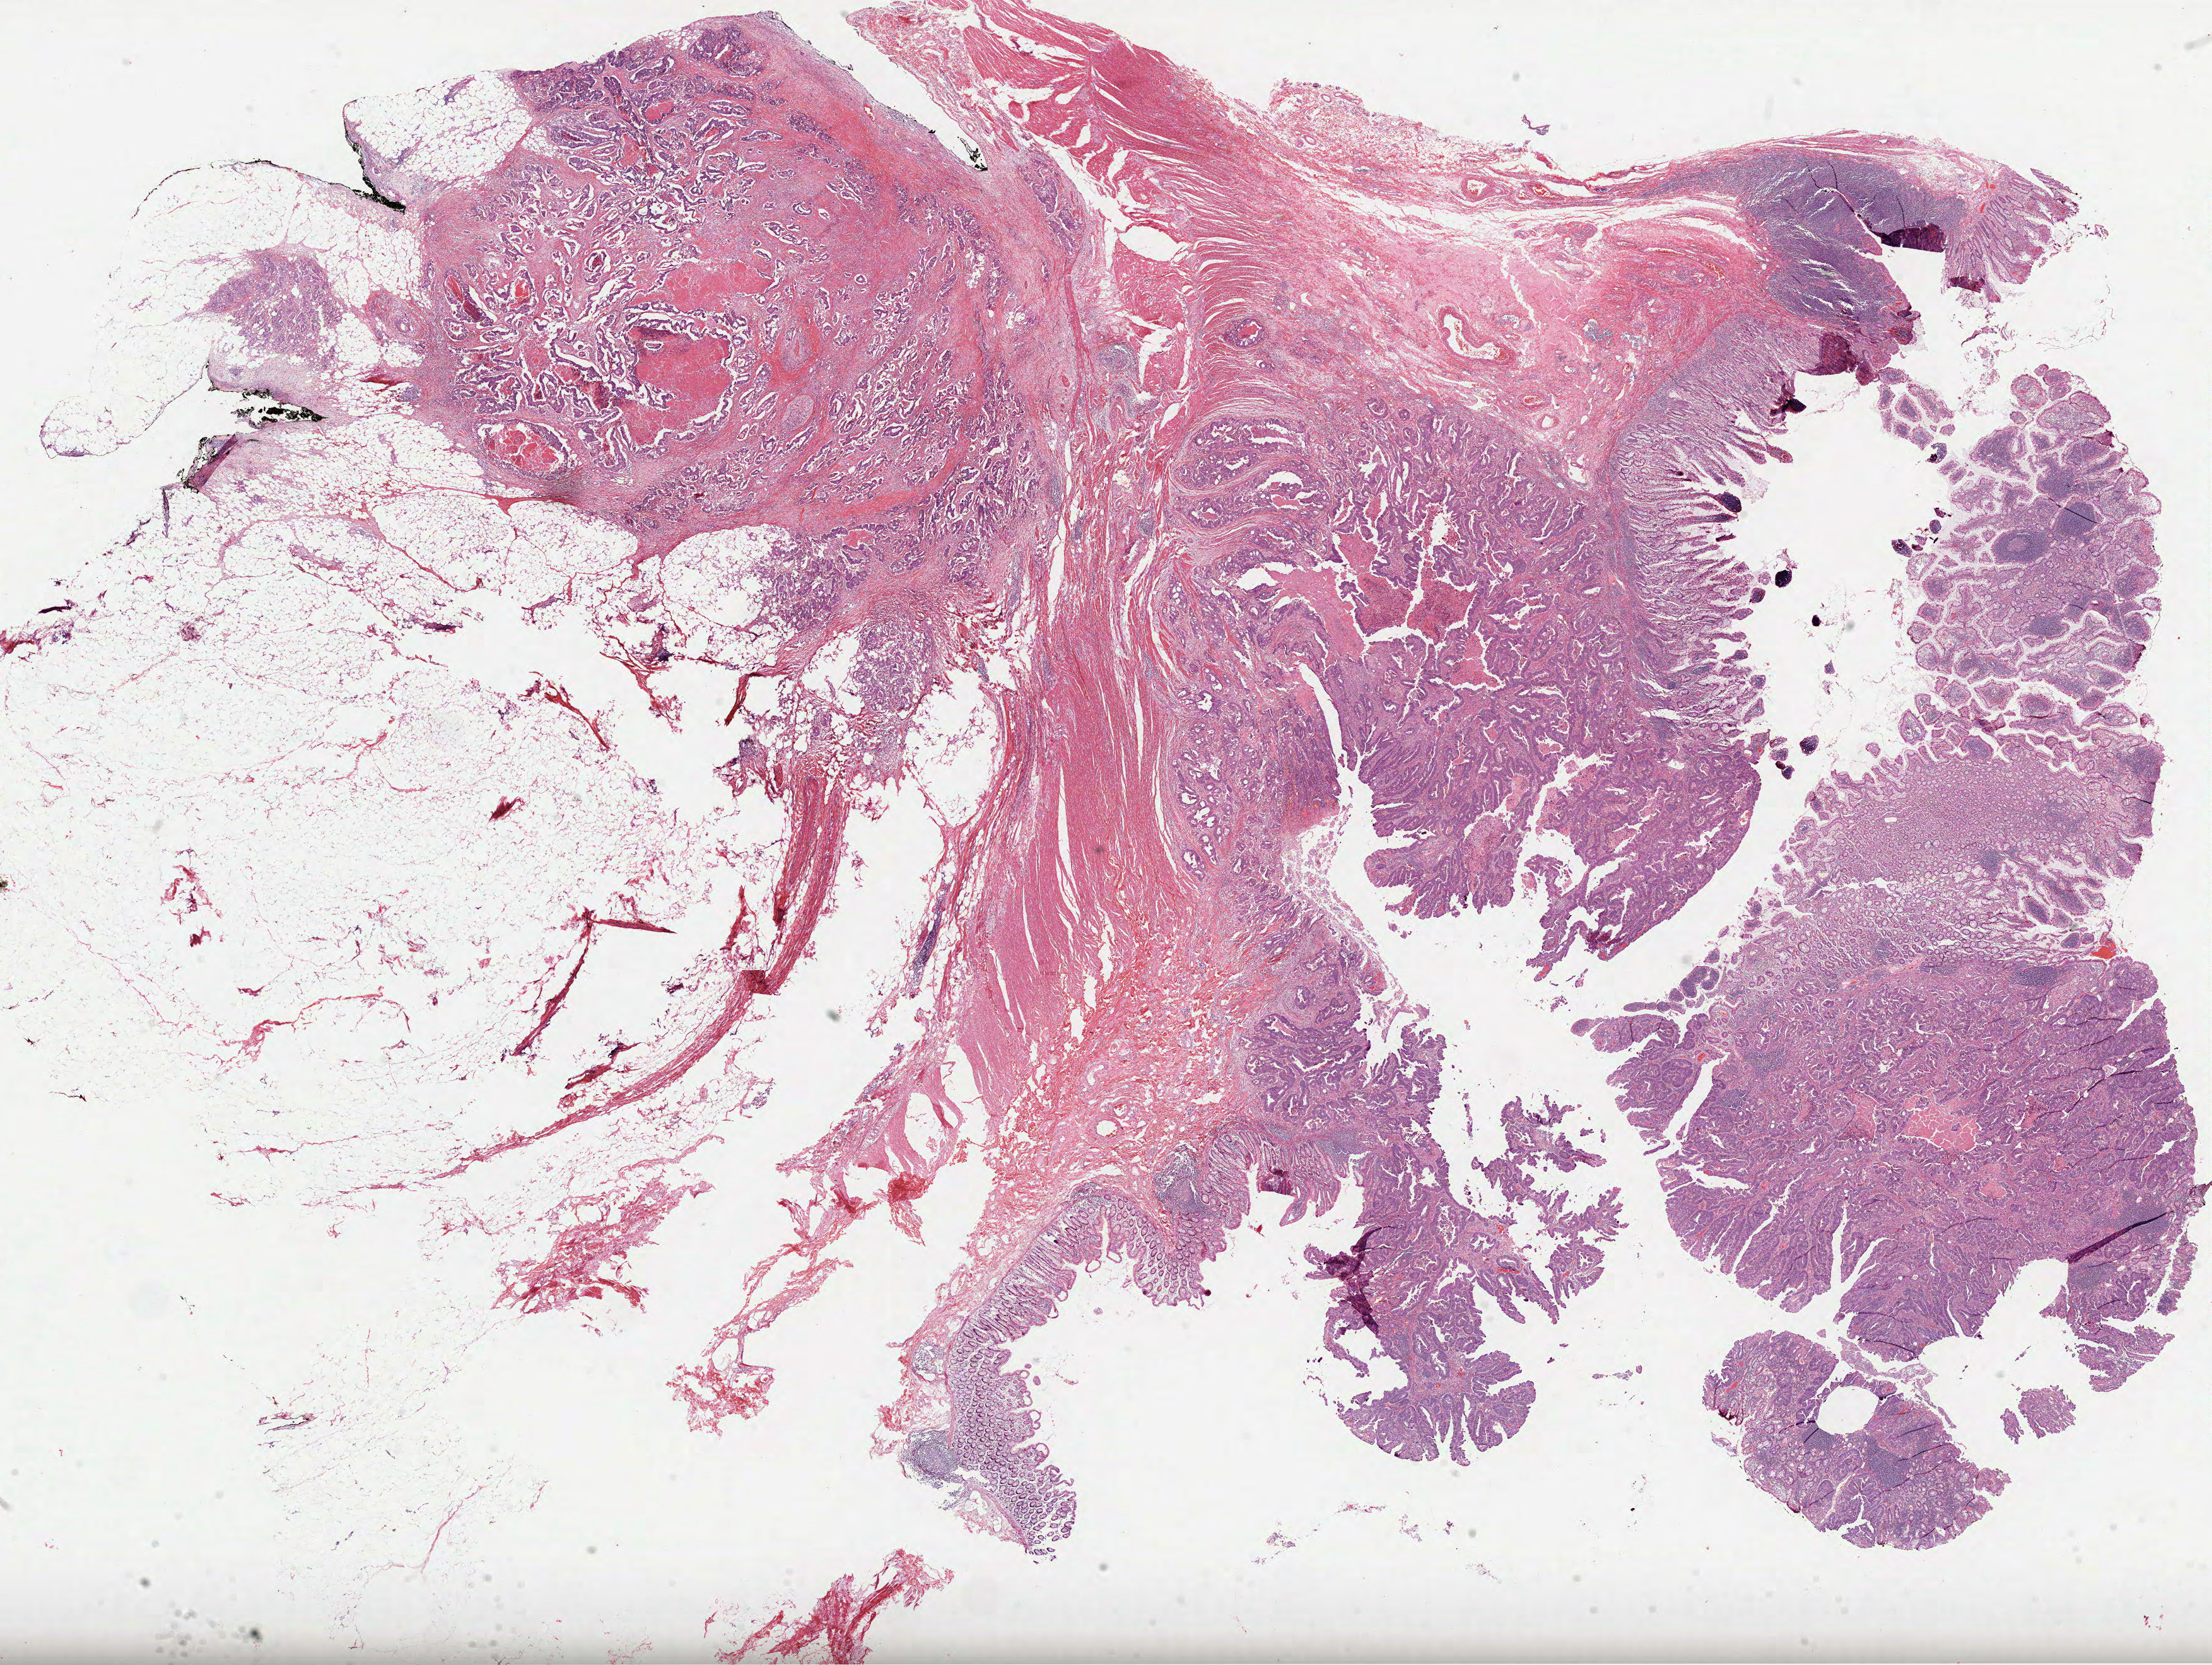
H&E-stained whole-slide image — low-resolution overview of the scanned area, about 28.3 x 21.3 mm (from a 40x scan). Formalin-fixed paraffin-embedded (FFPE) diagnostic section. Primary tumour sample from the colon. Patient: female, age at initial diagnosis 55 years.
- TNM: T3 N2 M1
- AJCC pathologic stage: IV
- histologic diagnosis: Adenocarcinoma, NOS (cecum)
- lymph nodes positive (case pathology): 6 of 36 examined